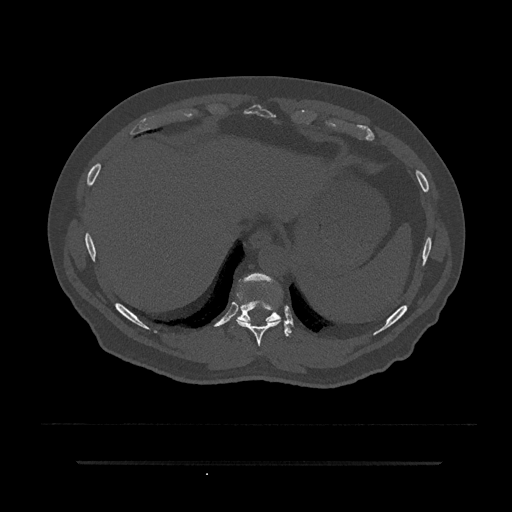
CT including the spine, one axial slice; position 355 of 797 along the scan axis; 120 kVp; bone window (W 1800 / L 400 HU); 0.5 mm slice thickness; 512 × 512 image matrix, field of view 464 × 464 mm. Male patient, age 59 years. Case-level facts recorded for this patient, not image findings: primary cancer: bile ducts; vertebrae with lytic lesions (as recorded): T10.
Outlined on this slice (semi-automatic segmentation, software-assisted and operator-edited):
- T10 vertebra: bounding box [x1, y1, x2, y2] px = [232, 273, 292, 337]
- T9 vertebra: [238, 307, 281, 346]